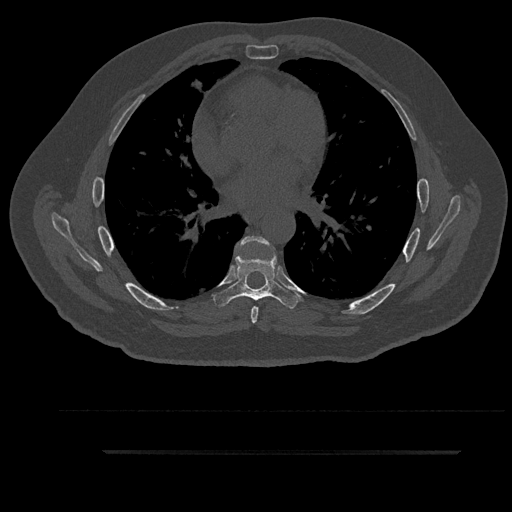
CT including the spine, one axial slice; position 543 of 797 along the scan axis; bone window (W 1800 / L 400 HU); 0.5 mm slice thickness; 512 × 512 image matrix, field of view 432 × 432 mm. Male patient, age 63 years. From the clinical record (not read from this slice): primary cancer: renal; vertebrae with lytic lesions (as recorded): T8.
Annotated regions visible in this slice (semi-automatically segmented with operator editing):
- T6 vertebra: bounding box <236,236,269,323> (left, top, right, bottom; pixels)
- T7 vertebra: <213,246,300,308>